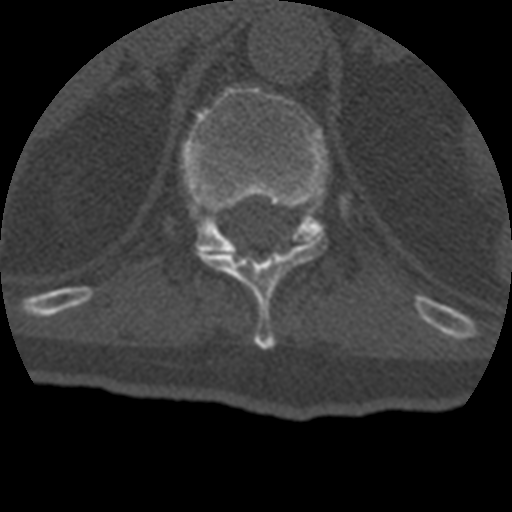
CT including the spine, one axial slice; position 185 of 399 along the scan axis; reconstruction kernel STANDARD; 120 kVp; bone window (W 1800 / L 400 HU); 1.25 mm slice thickness; 512 × 512 image matrix. Patient age 69 years. From the clinical record (not read from this slice): primary cancer: prostate.
Structures marked on this image (semi-automatically segmented with operator editing):
- T11 vertebra: bounding box (x1, y1, x2, y2) in pixels: (204, 236, 328, 349)
- T12 vertebra: (181, 86, 330, 252)